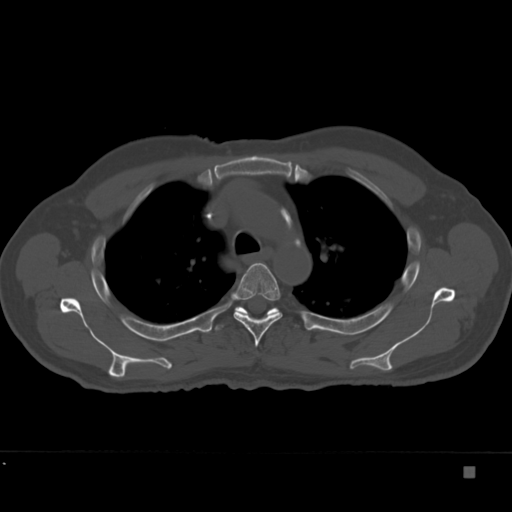
CT including the spine, one axial slice; slice 268 of 332 in the series (ordered by position); 120 kVp; bone window (W 1800 / L 400 HU); 512 × 512 image matrix. Patient: male, 72 years. From the clinical record (not read from this slice): primary cancer: skeletal.
Annotated regions visible in this slice (semi-automatic segmentation, software-assisted and operator-edited):
- T4 vertebra: bounding box [x1, y1, x2, y2] px = [231, 263, 283, 347]
- T5 vertebra: [217, 306, 276, 330]